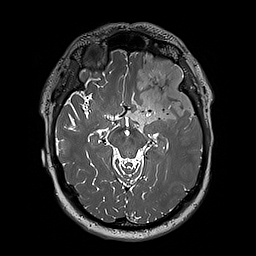
Brain MRI from a brain-tumour surgery series, one axial slice; slice 125 of 192 in the series (ordered by position); 1 mm slice thickness; 256 × 256 image matrix, field of view 250 × 250 mm. From the clinical record (not read from this slice): histopathology: Oligodendroglioma; WHO grade: 3; IDH mutation: yes.
Structures marked on this image (manually delineated by an expert):
- tumour: box from (x=124, y=55) to (x=197, y=125) px